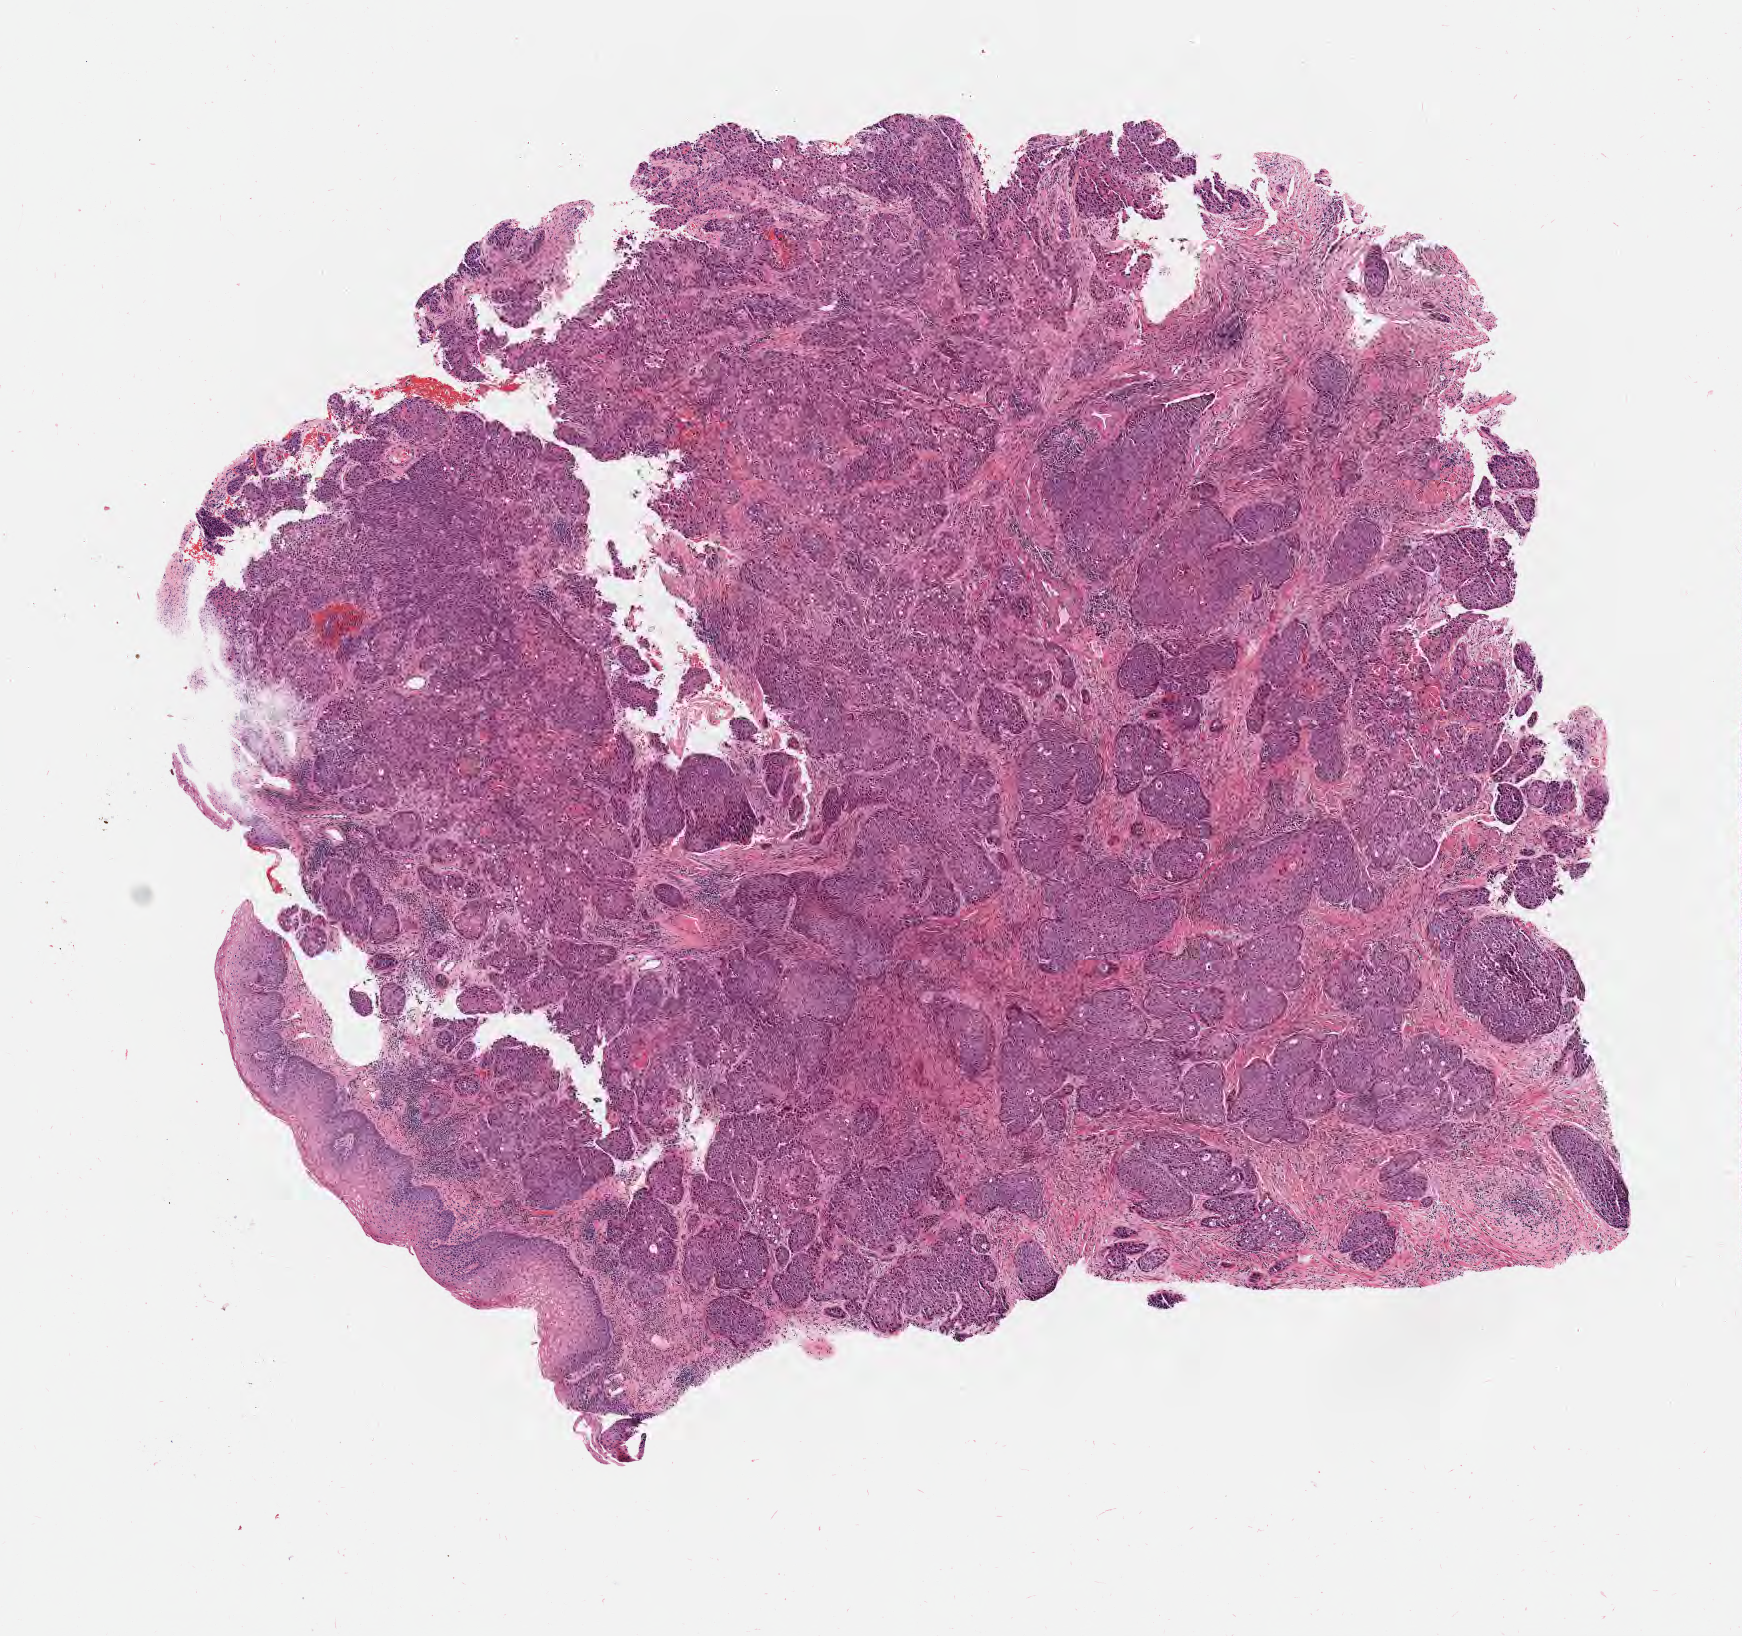
Digitized haematoxylin and eosin-stained section — low-resolution overview of the scanned area, about 7.0 x 6.6 mm; tumor tissue; anatomic site: cervix. Female patient, 47 years old.
* diagnosis: Squamous cell carcinoma, keratinizing, NOS